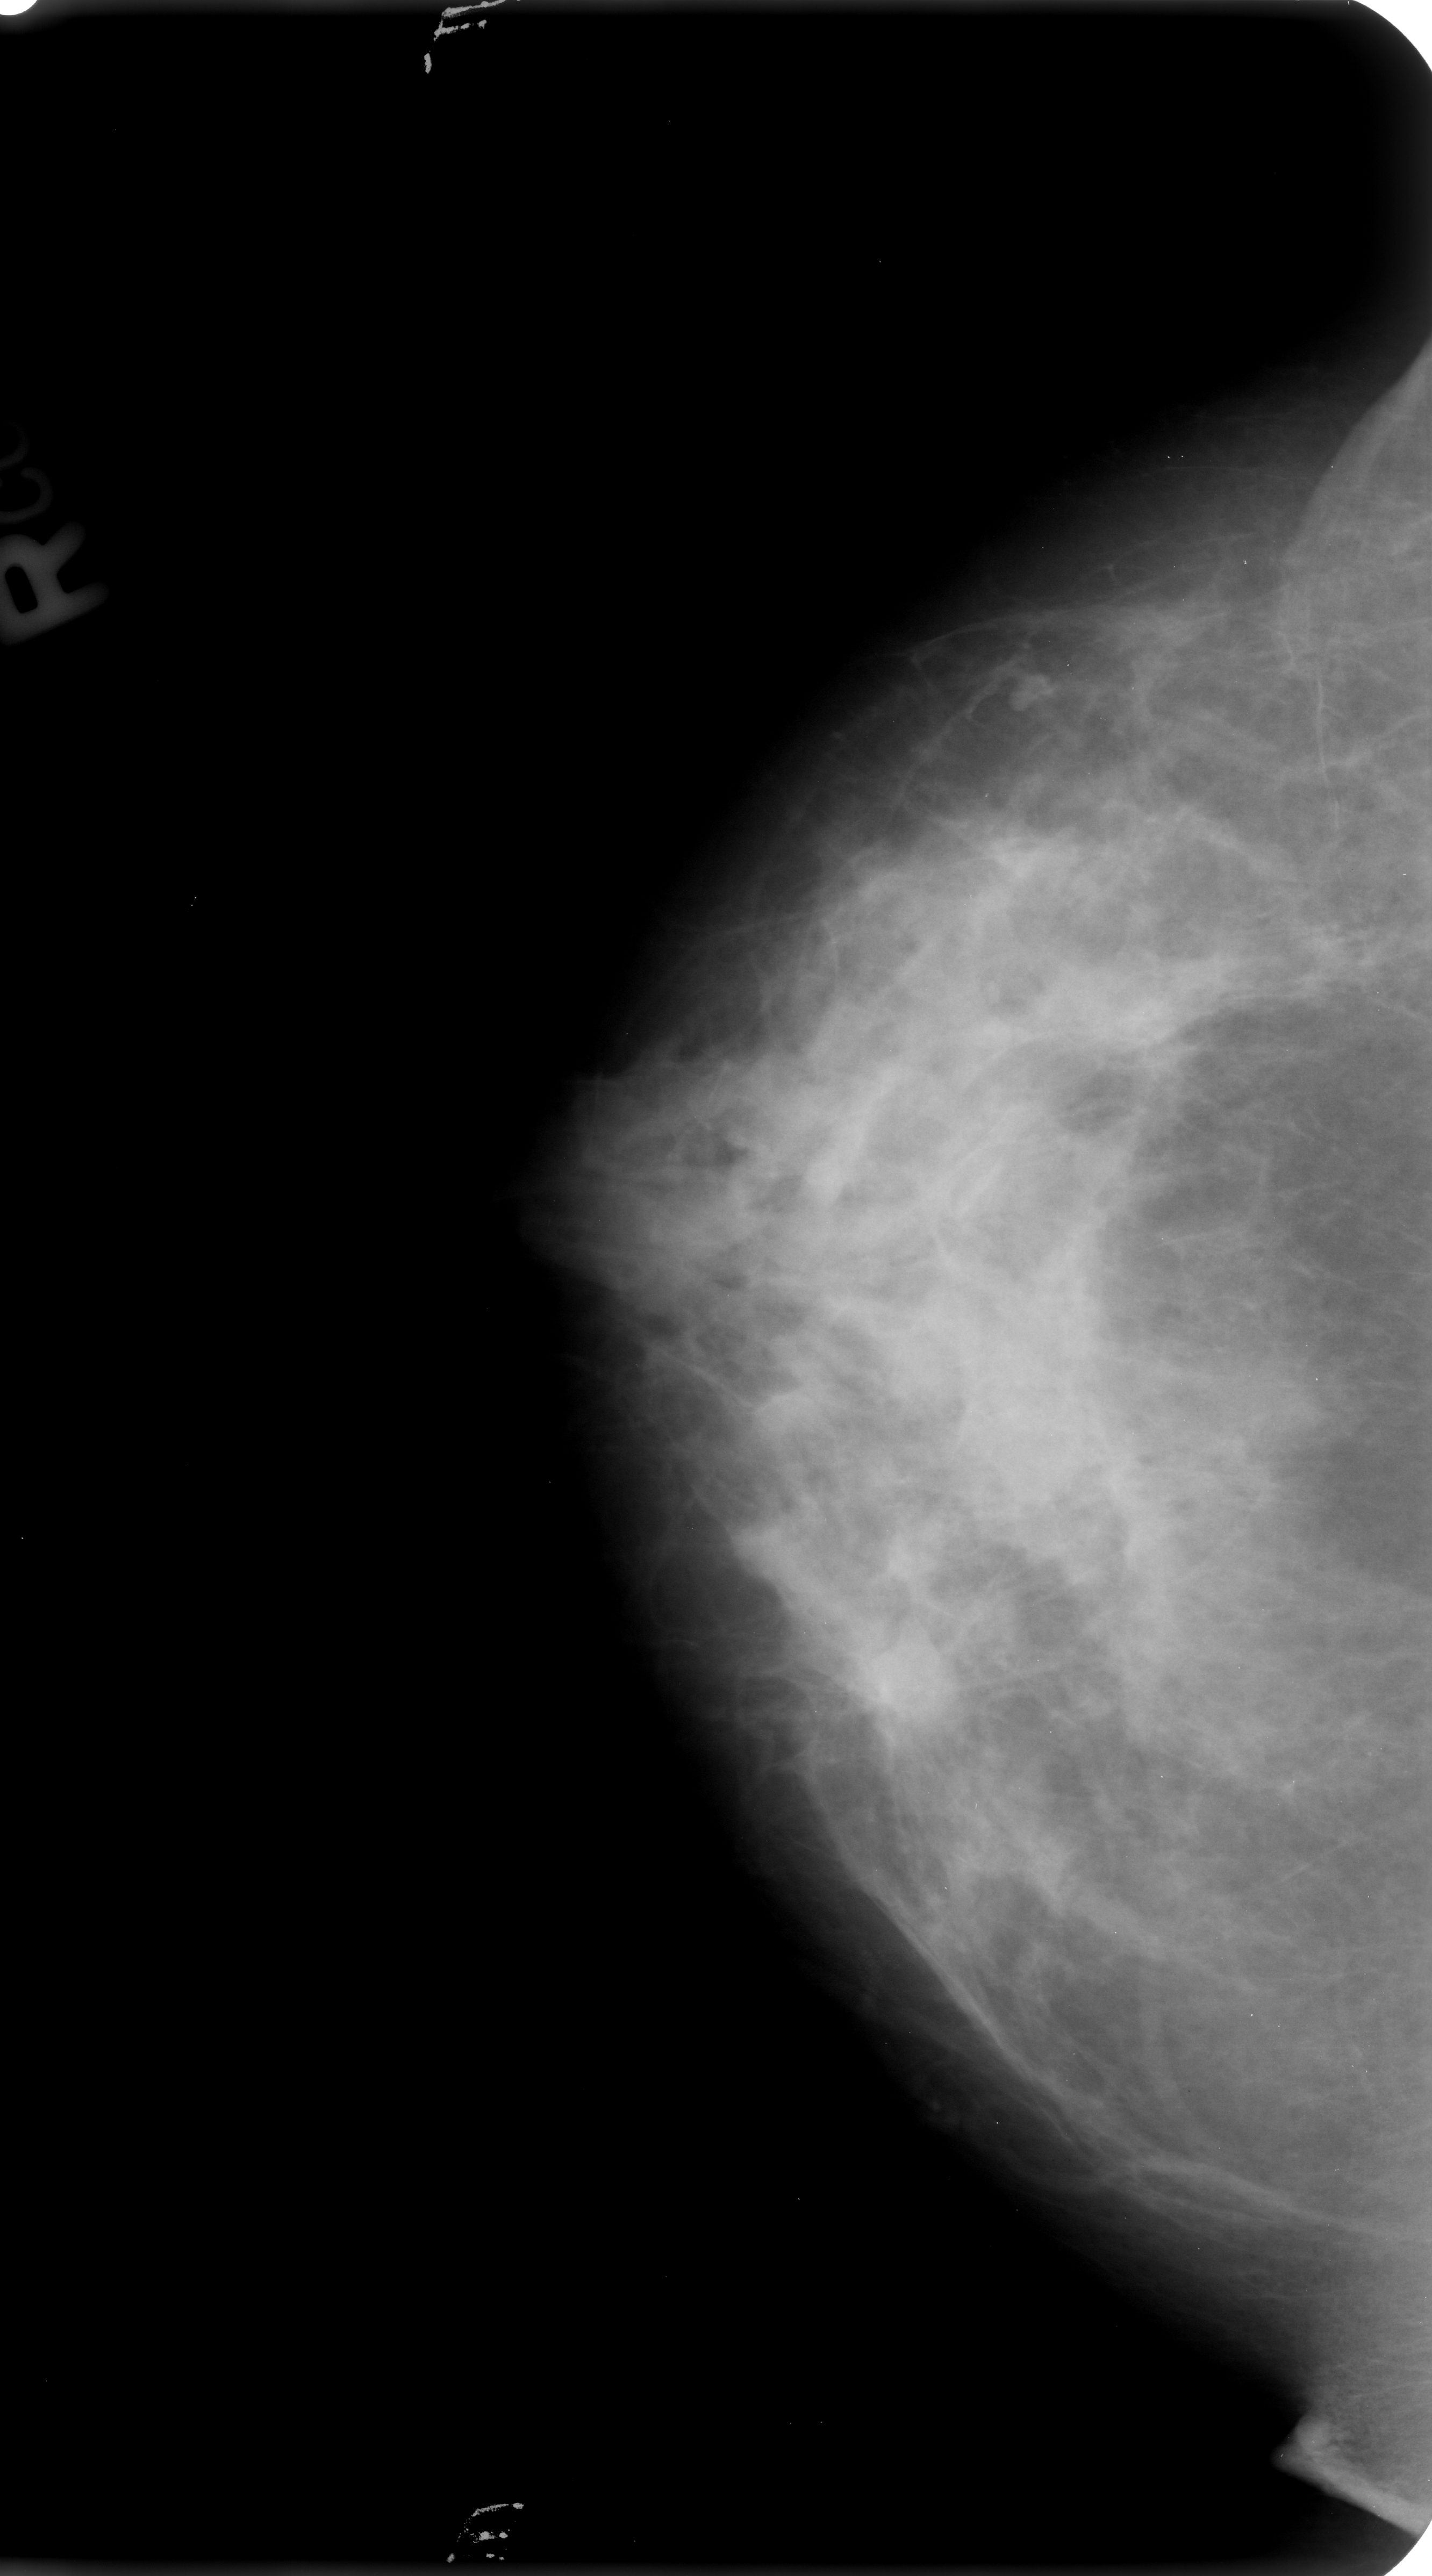
Scanned film-screen mammogram. Right breast. Craniocaudal (CC) view. Breast composition: heterogeneously dense (BI-RADS density category 3 of 4). 1432 × 2576 image matrix.
Expert-marked regions of interest on this image (one box per marked abnormality):
- mass, shape irregular, margins ill defined / spiculated; BI-RADS assessment category 4; subtlety rating 2 on a 1 (subtle) to 5 (obvious) scale; pathology result (as recorded, not read from the image): benign: bounding box (x1, y1, x2, y2) in pixels: (833, 1618, 973, 1771)